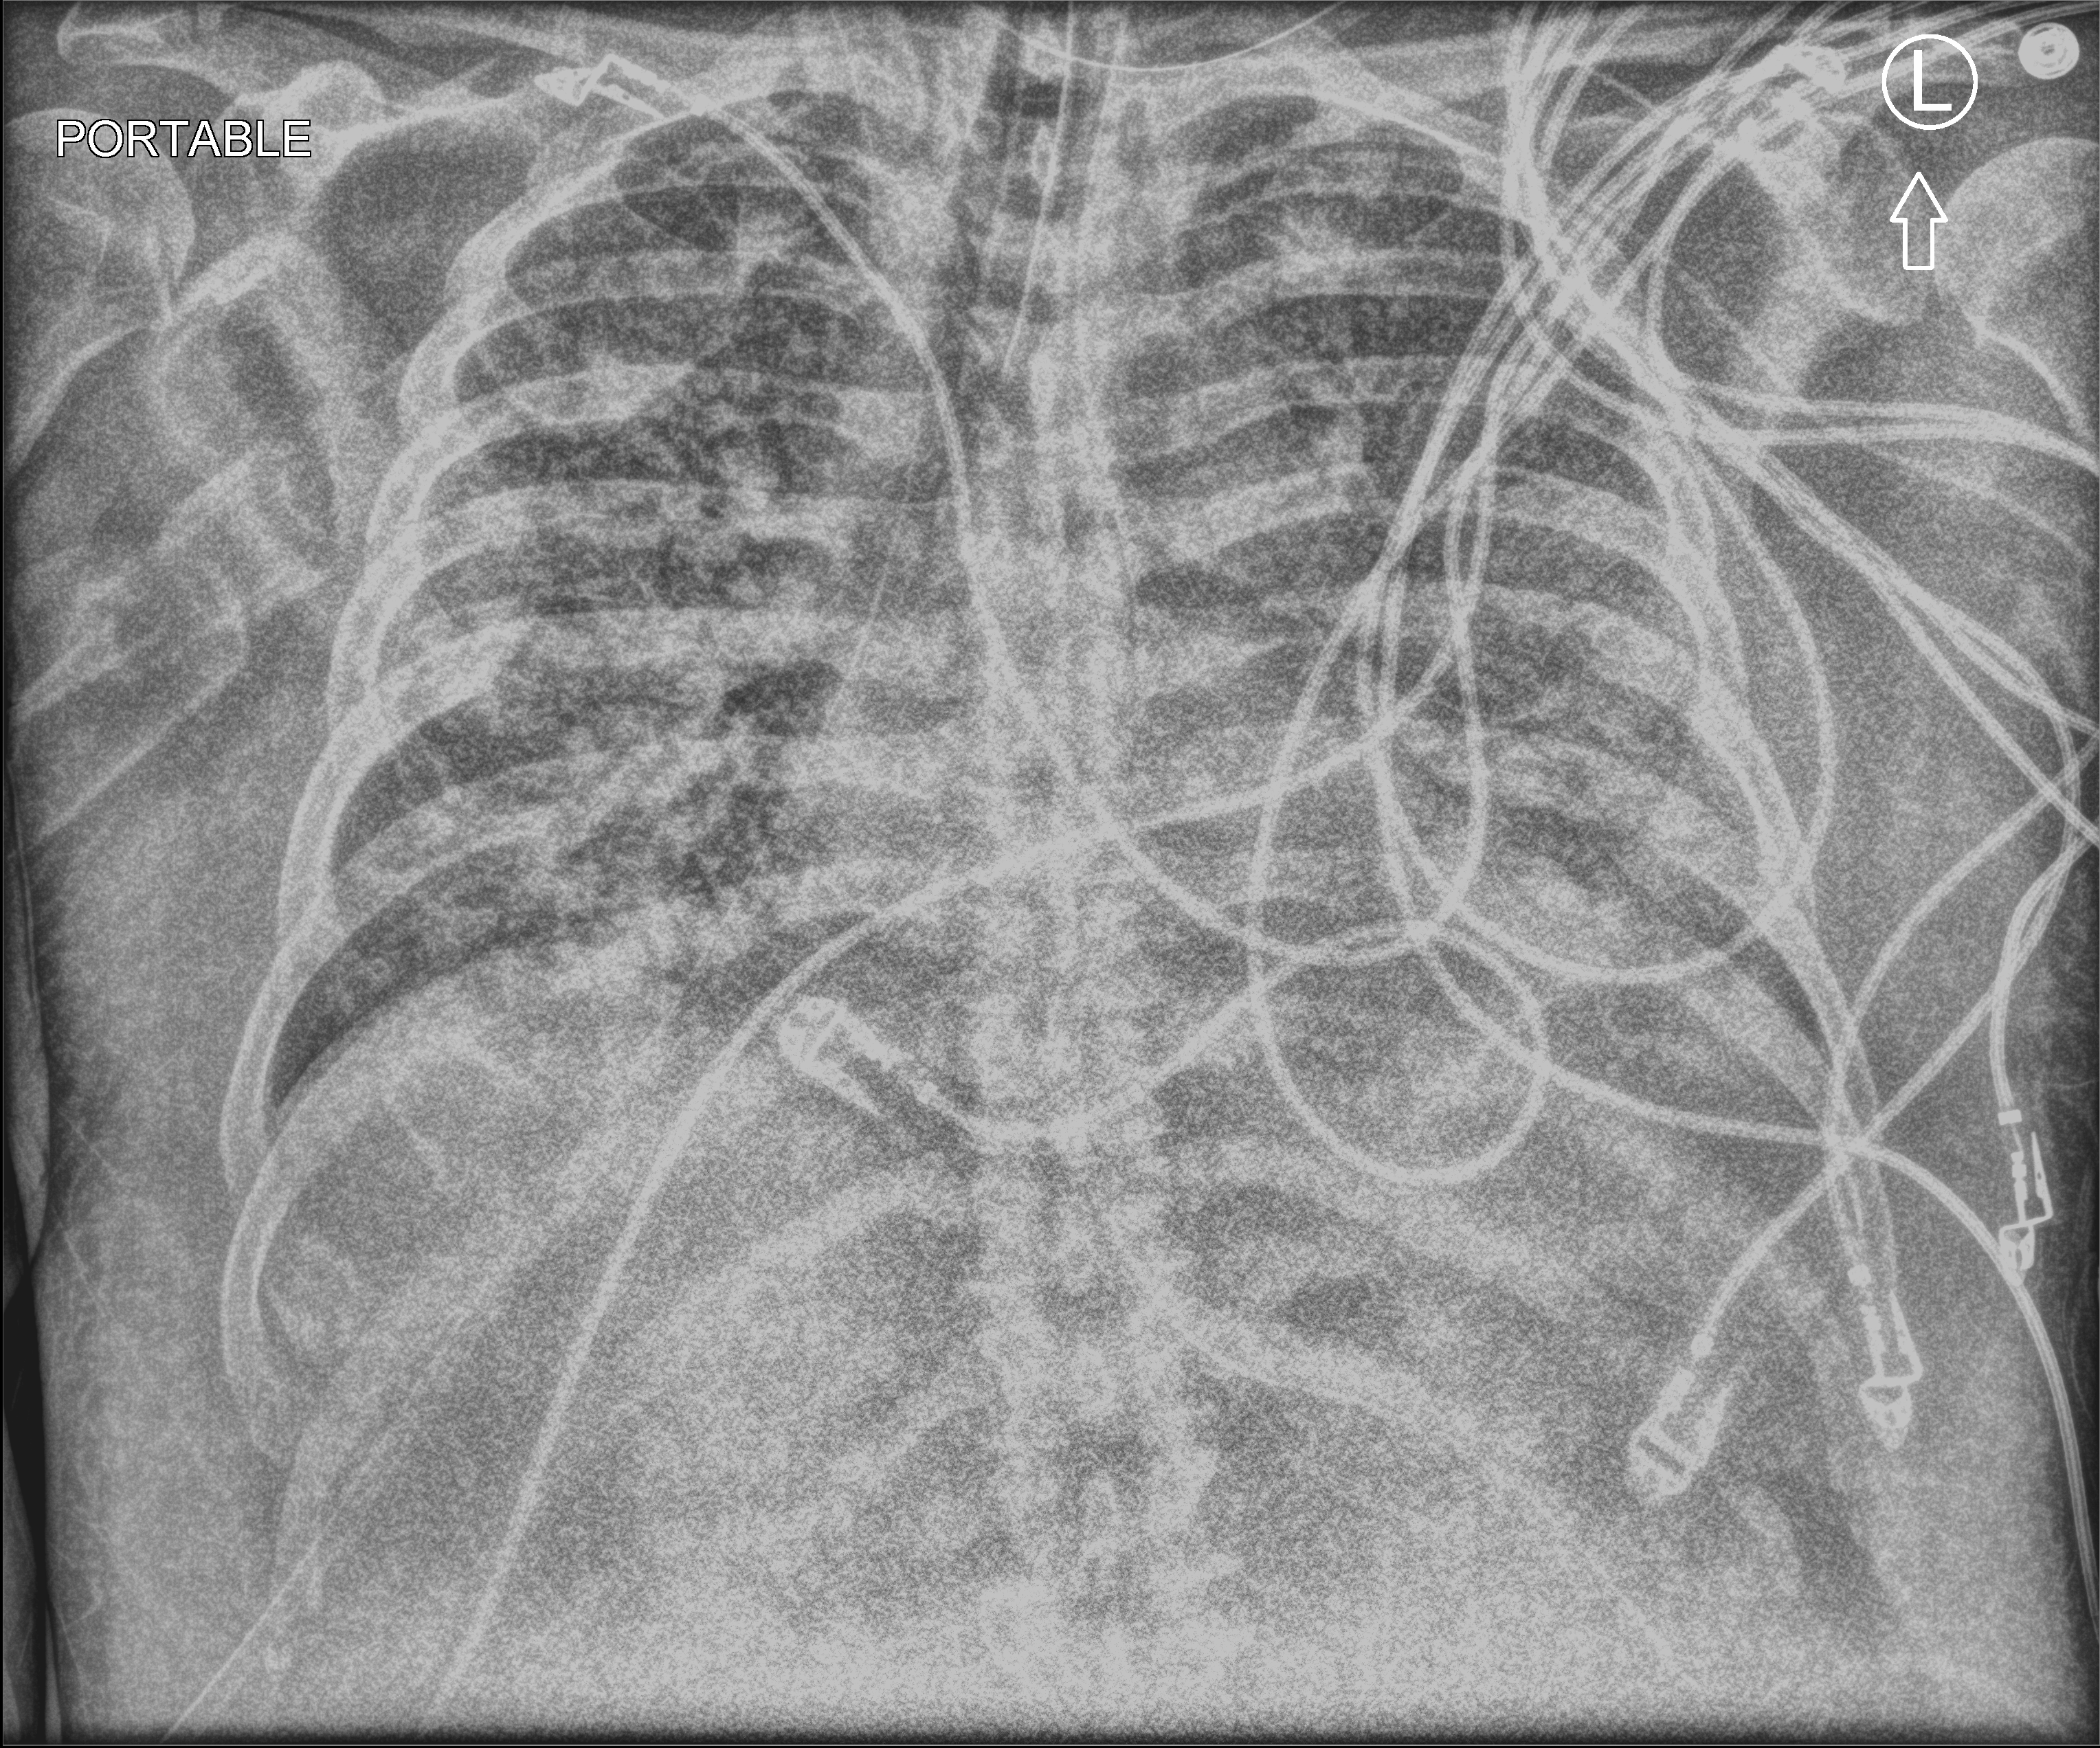
Chest X-ray (portable), anteroposterior (AP) projection. Male patient hospitalised with COVID-19, age 60–74 years.
From the hospital-stay record, not from the radiograph (when in the stay this image was taken is not recorded): length of hospital stay: 28 days.